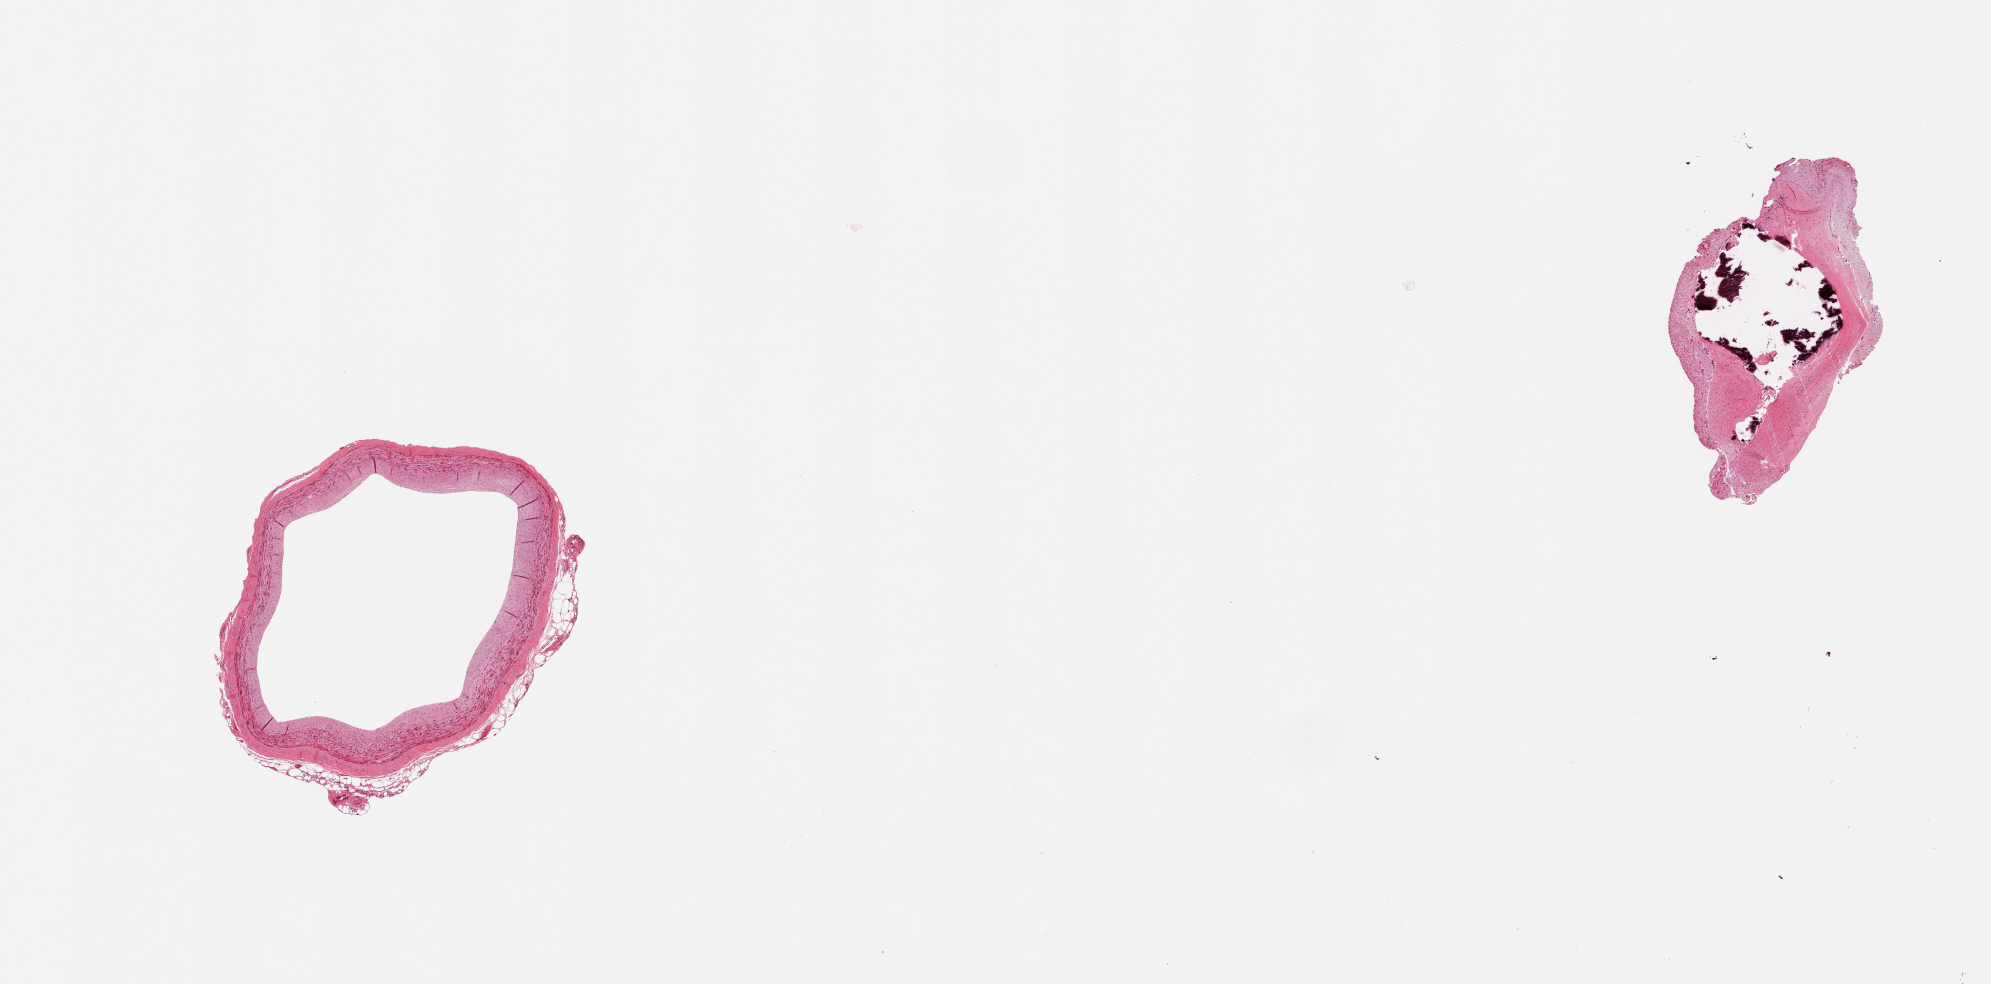
Whole-slide image, hematoxylin and eosin (H&E) stain, brightfield, shown as a low-resolution overview of the whole scanned area (about 15.8 x 7.8 mm), PAXgene-fixed, paraffin-embedded tissue, target tissue: coronary artery, tissue donor sample. Male donor.
Pathologist's review note for this sample: 2 pieces; calcific atherosclerosis.